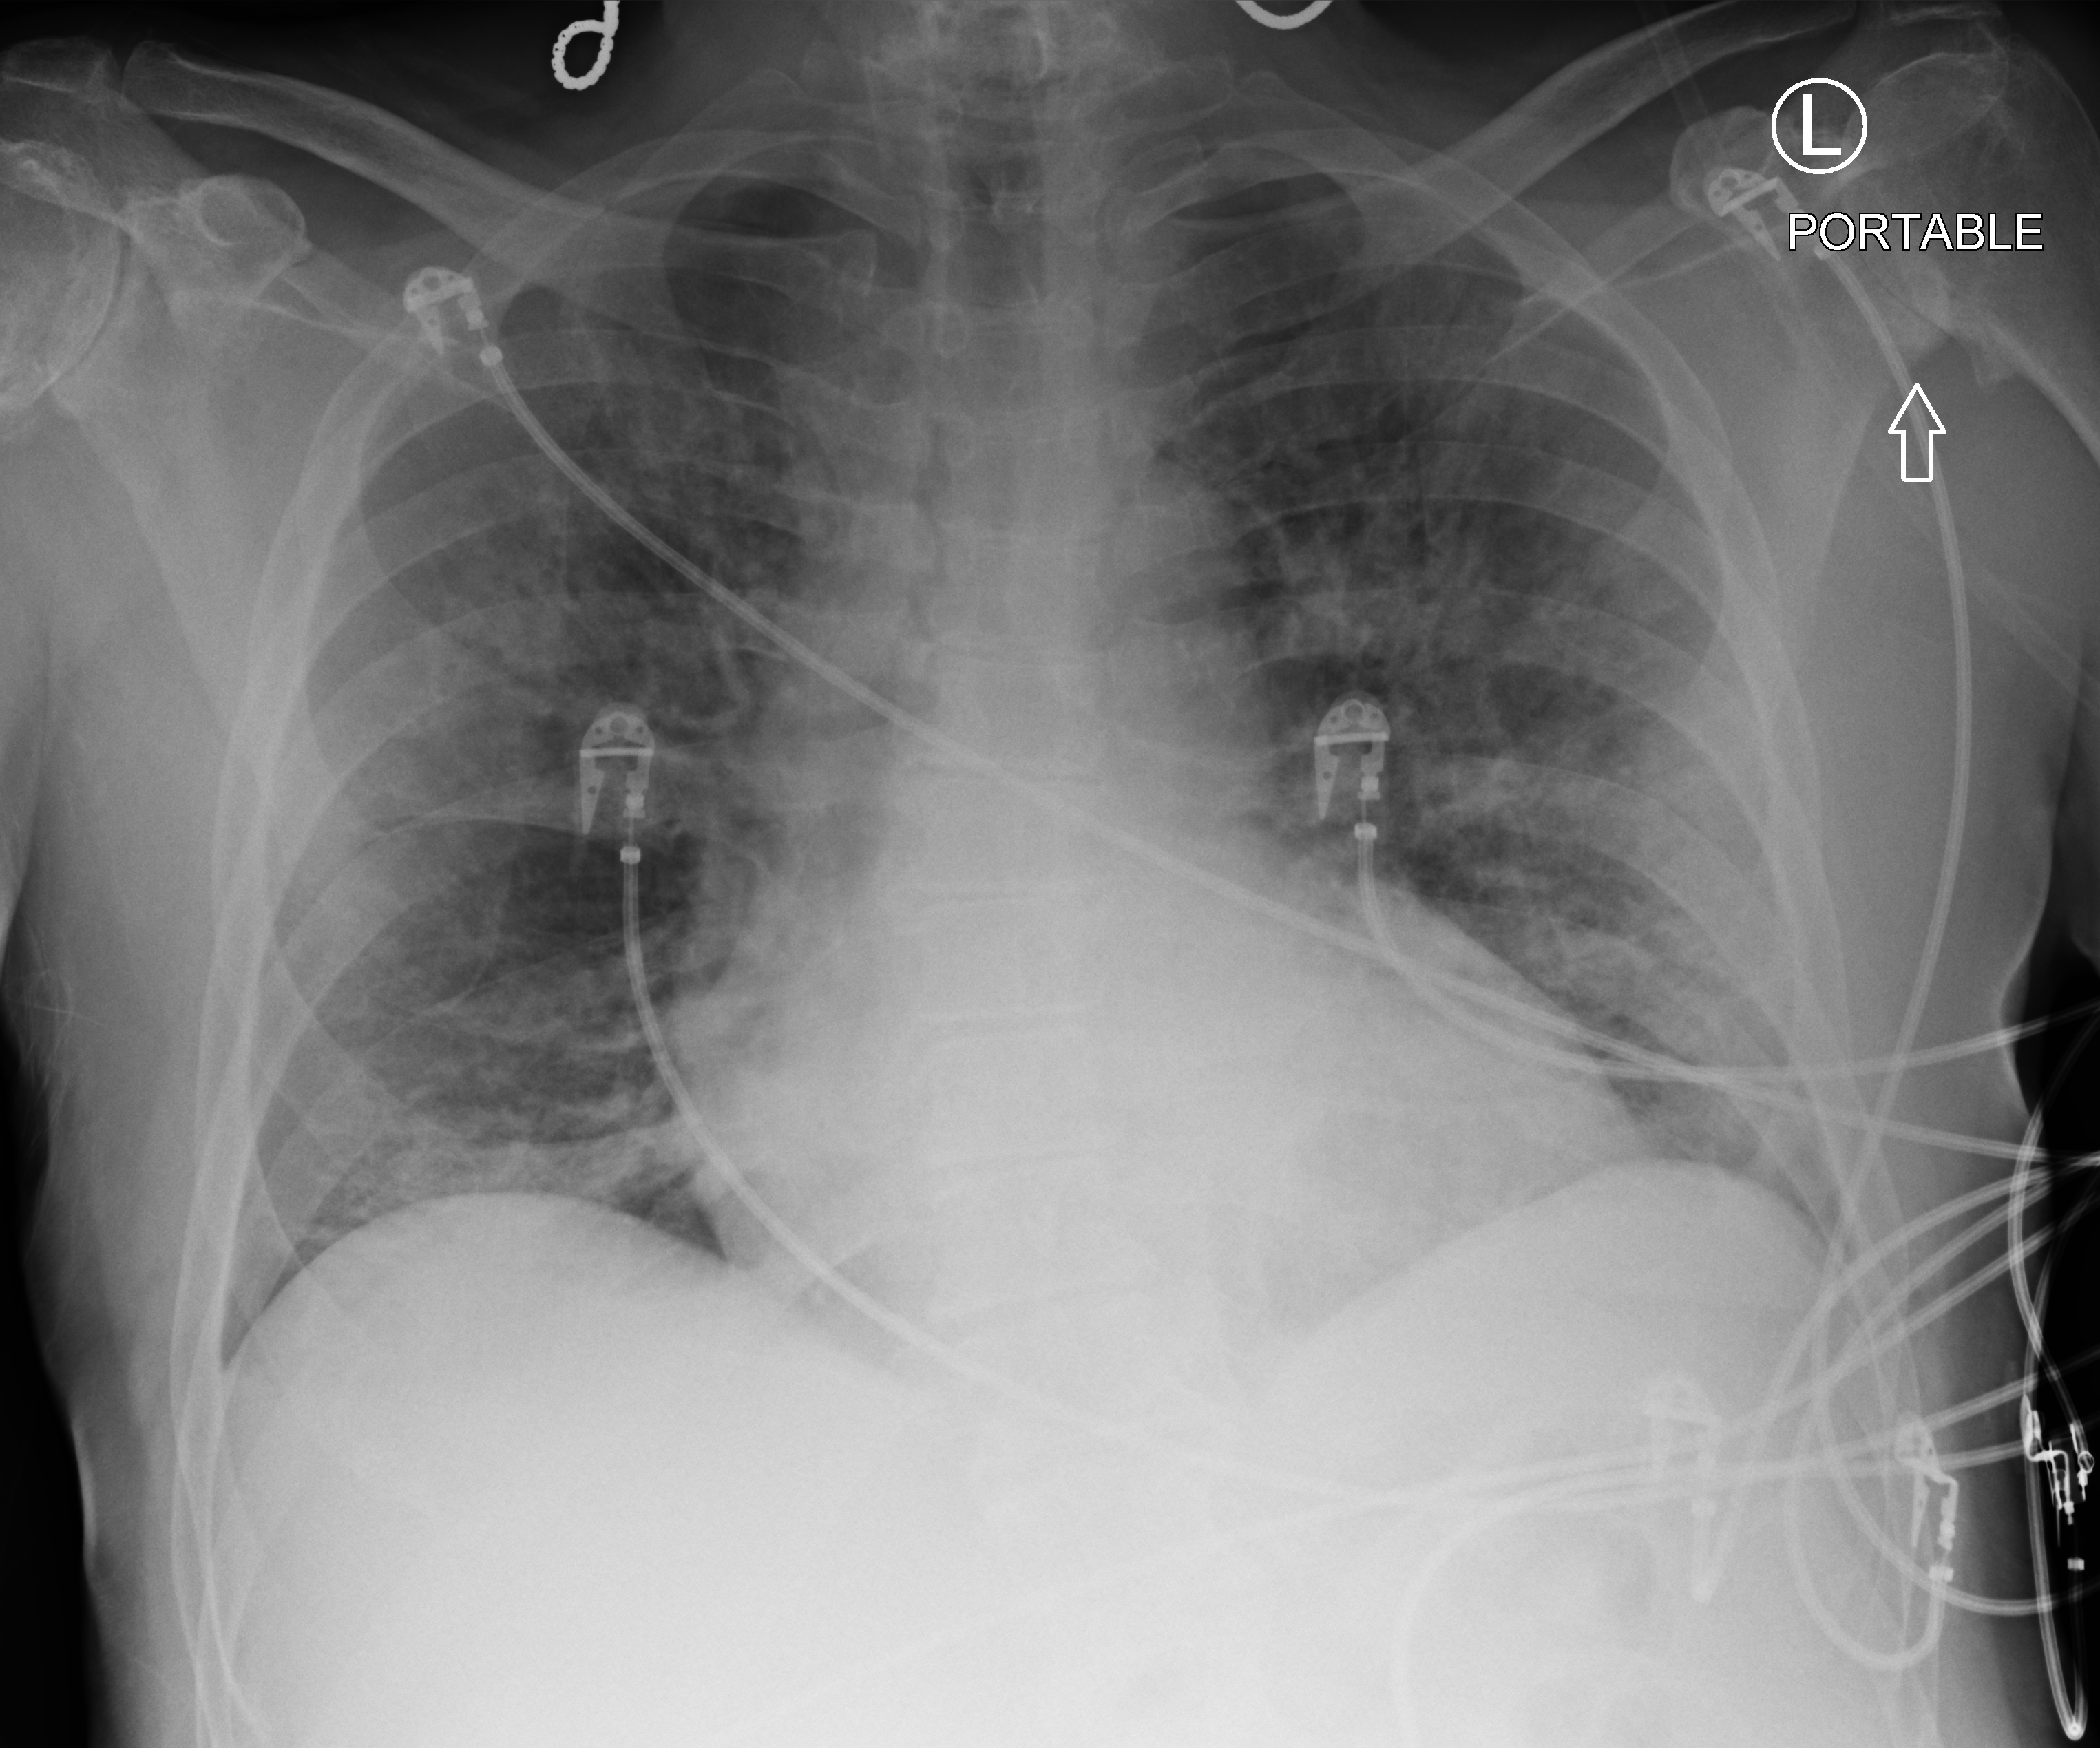
Portable chest radiograph. Patient hospitalised with COVID-19; male, aged 60–74 years.
Hospital-stay facts (about this admission, not read from this image; timing relative to this image not recorded): diabetes (admission record): no; chronic kidney disease (admission record): no.